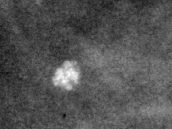
Cropped region of a digitized screen-film mammogram centred on a radiologist-marked abnormality; right breast; CC view; BI-RADS breast density category 1 (scale 1–4).
- Finding: mass, shape lymph node, margins circumscribed; BI-RADS assessment category 2; benign without callback (not worked up further).